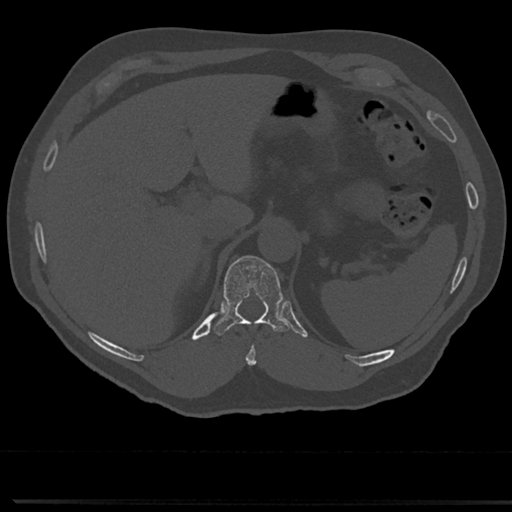
CT including the spine, one axial slice; slice 212 of 817 in the series (ordered by position); reconstruction kernel Br40s/3; bone window (W 1800 / L 400 HU); 0.5 mm slice thickness; 512 × 512 image matrix, field of view 355 × 355 mm. Male patient, age 61 years. Case-level facts recorded for this patient, not image findings: primary cancer: prostate.
Structures marked on this image (semi-automatically segmented with operator editing):
- T10 vertebra: box from (x=246, y=331) to (x=259, y=366) px
- T11 vertebra: (x=214, y=256)–(x=289, y=336)